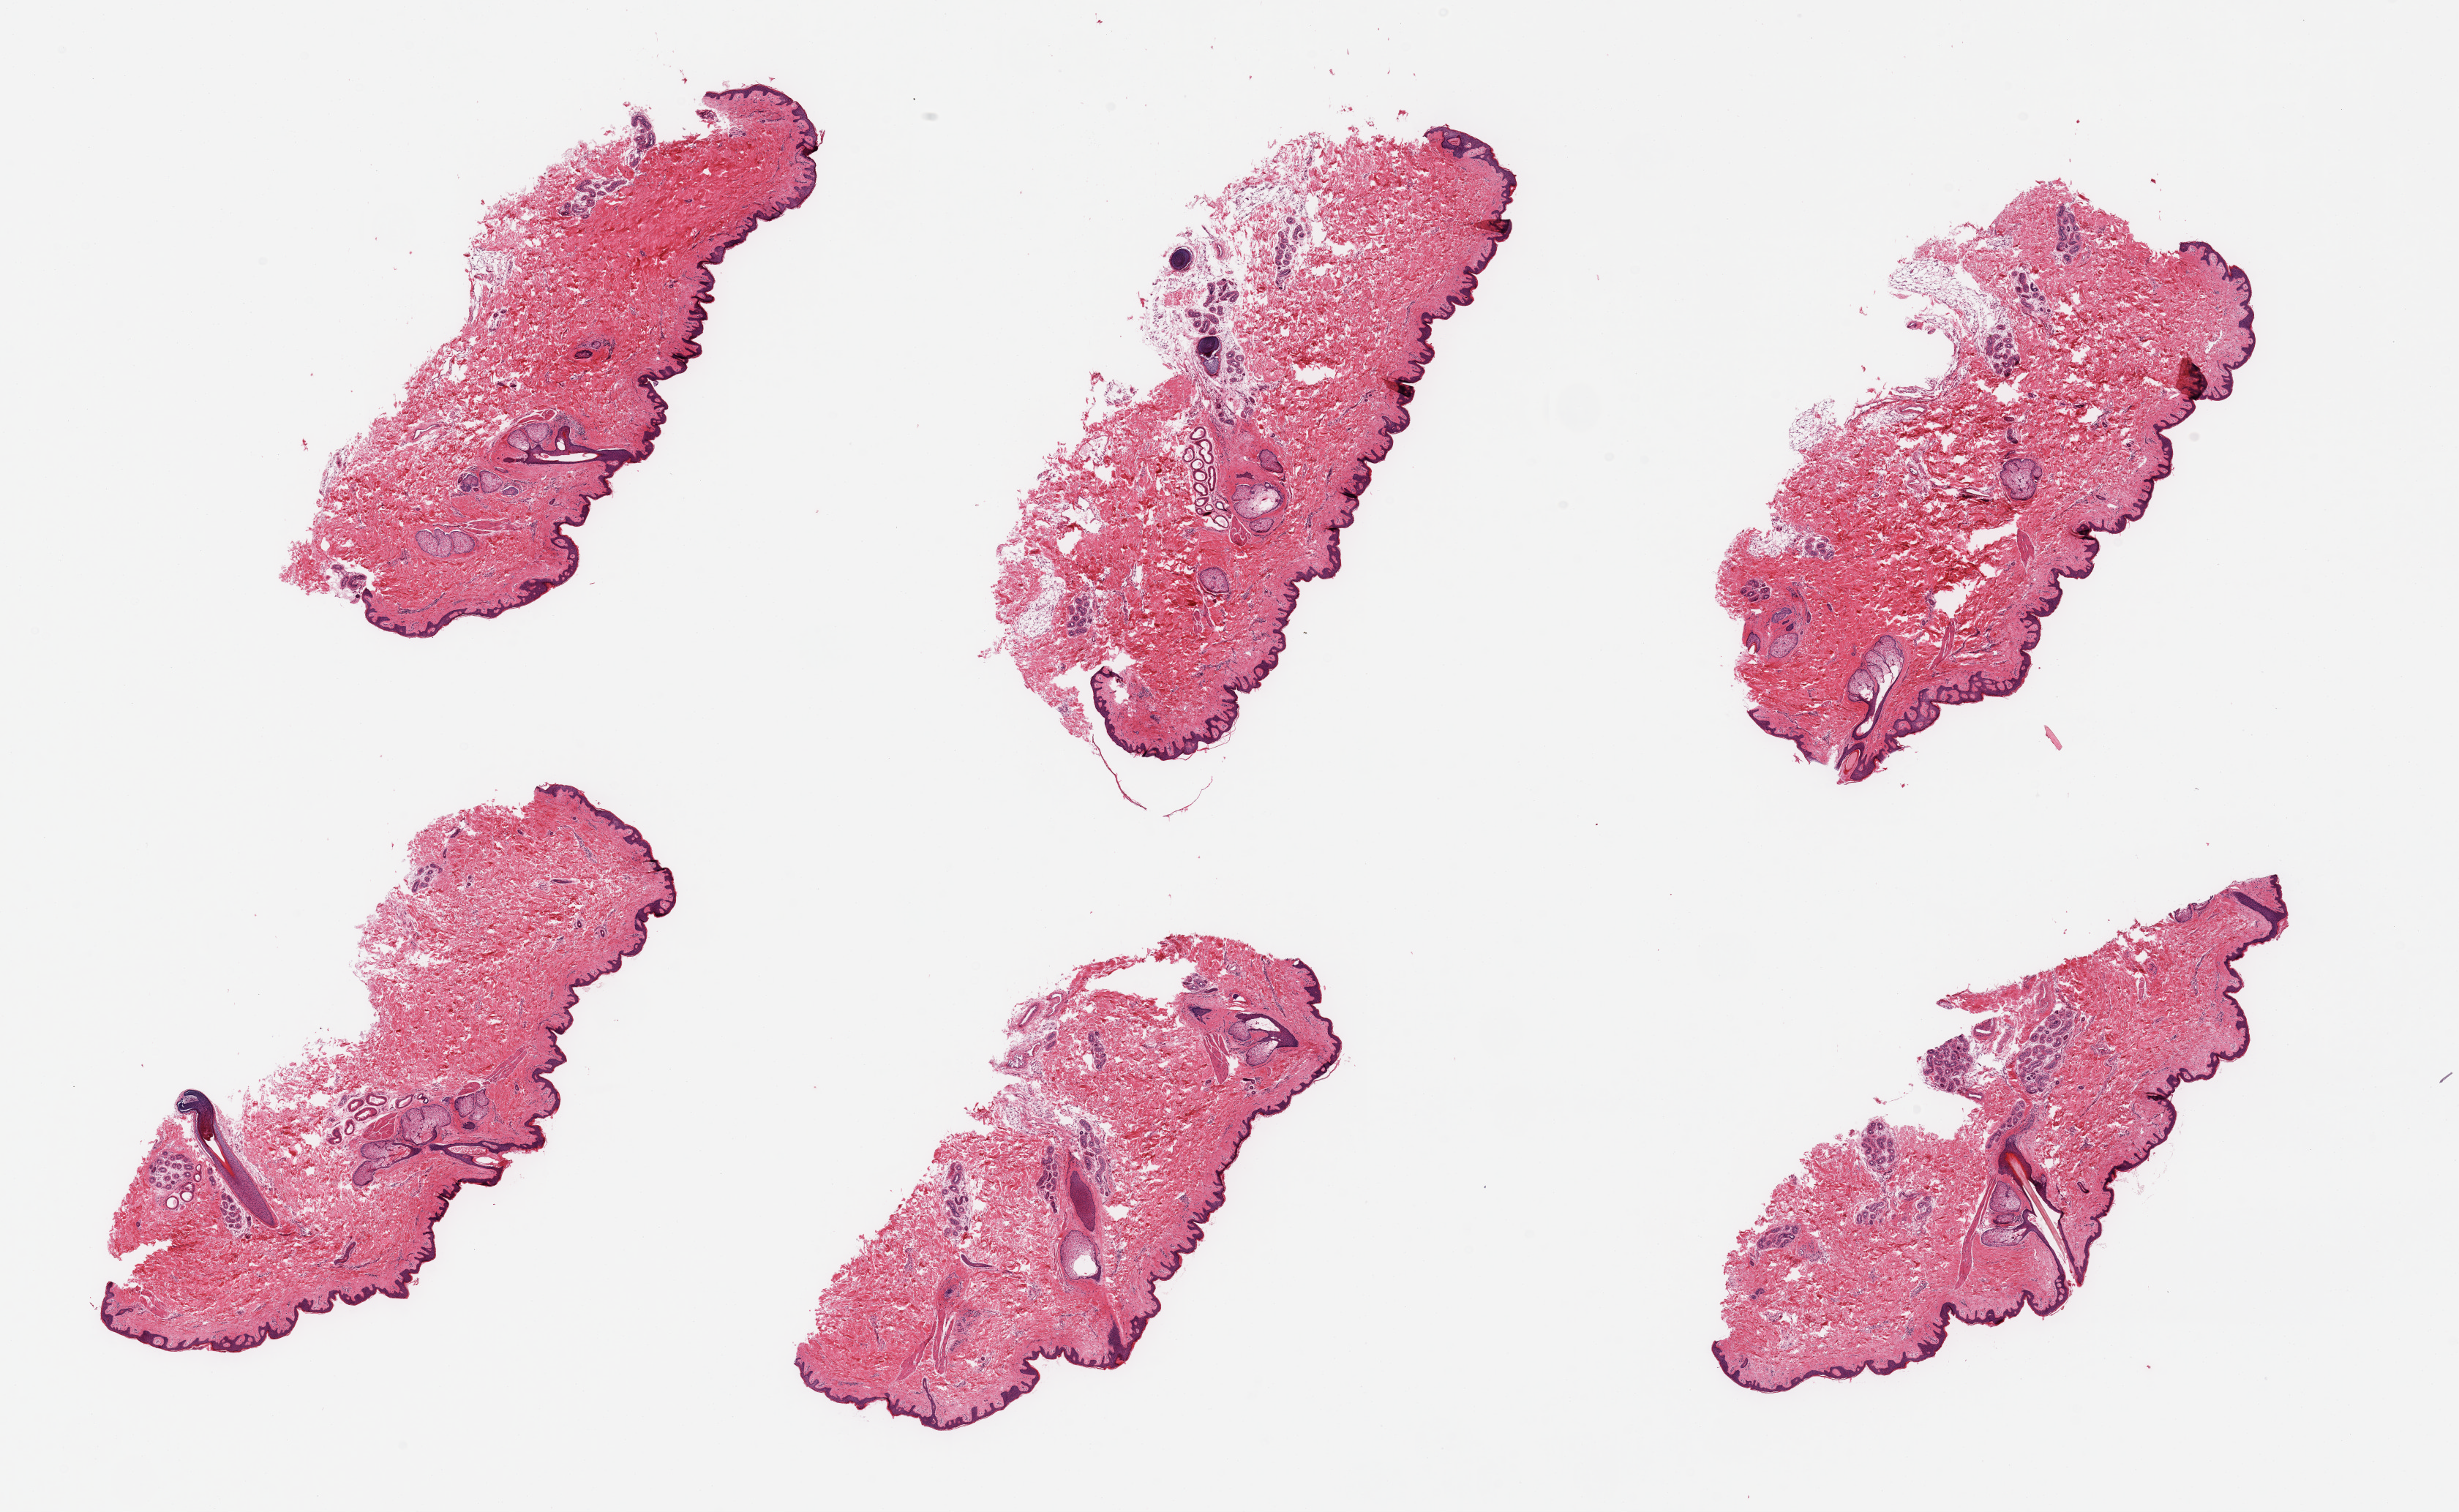
H&E whole-slide image, brightfield, low-resolution overview of the scanned area, about 26.6 x 16.3 mm. PAXgene-fixed, paraffin-embedded tissue. Sampled site (target tissue): skin of suprapubic region. Tissue donor sample. Male donor.
Pathologist's review note for this sample: 6 pieces; well trimmed; contains several hair follicles.